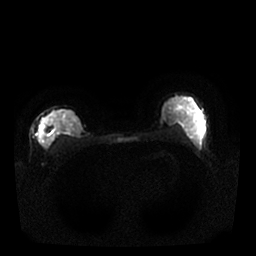
Breast MRI, one axial slice; position 16 of 25 along the scan axis; diffusion-weighted series; image 2 of 4 stored at this slice position (different b-values; order by instance number); 1.5 T; 256 × 256 image matrix, field of view 340 × 340 mm. Female patient.
Annotated regions visible in this slice (expert manual segmentation):
- tumour on diffusion-weighted imaging: bounding box [x1, y1, x2, y2] px = [41, 125, 47, 139]